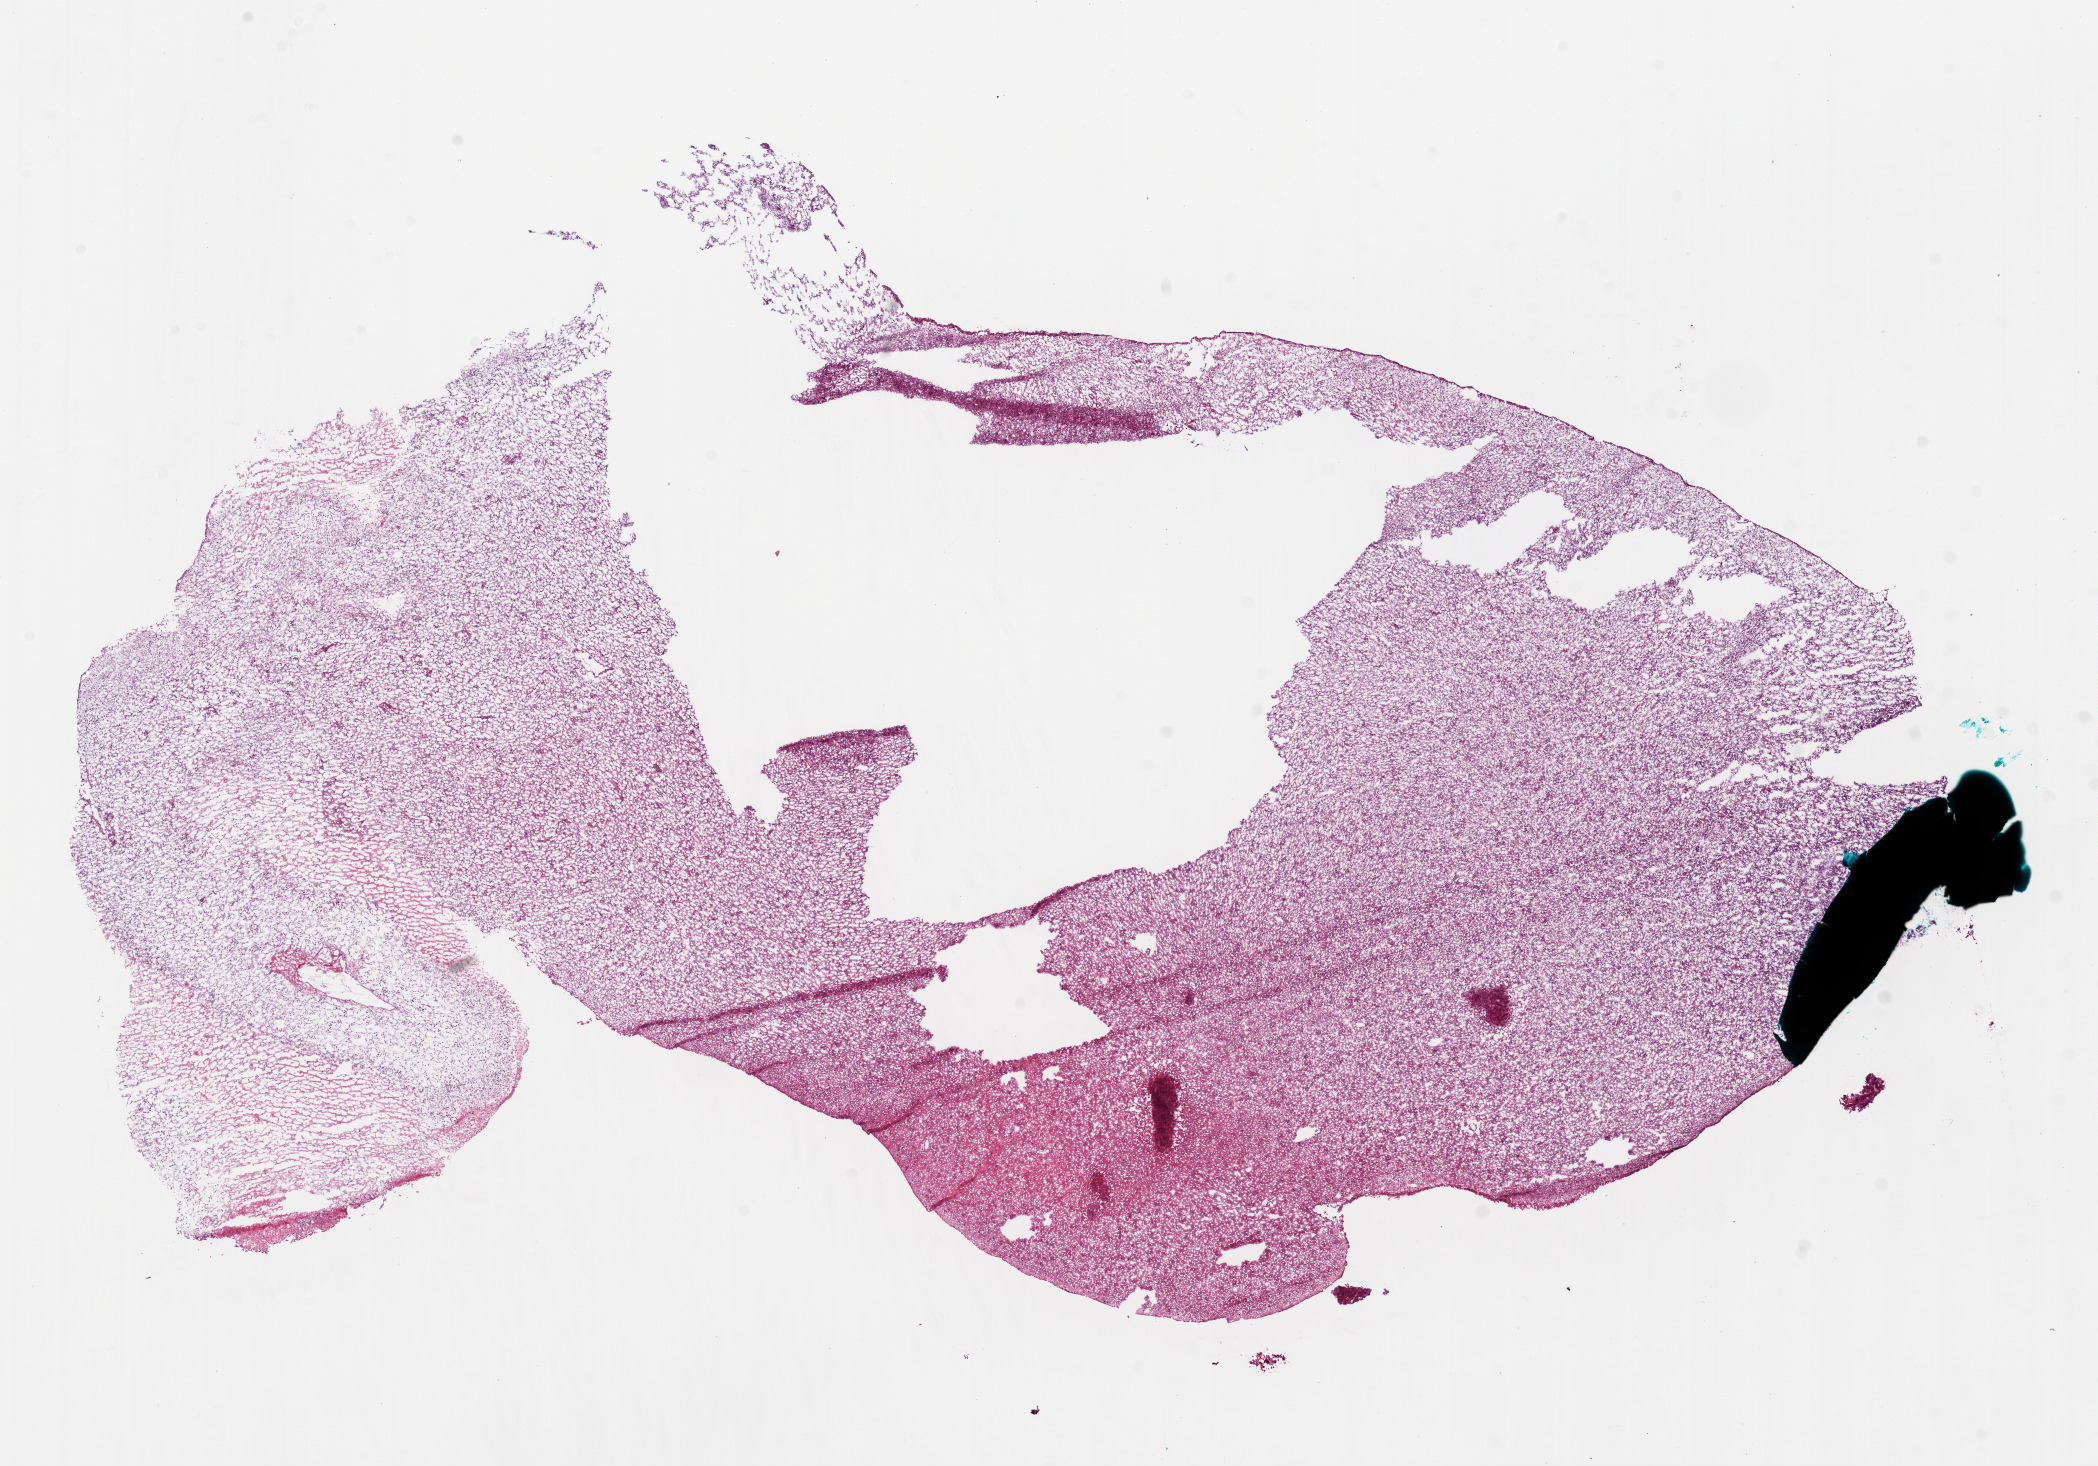
Digitized H&E tissue section (whole slide), a low-resolution overview of the entire scanned area, about 16.9 x 11.8 mm (acquisition: 20x scan), frozen section from the bottom of the tissue portion, brain, primary tumour sample. Female patient; age at initial diagnosis 51 years. Composition of this section per pathologist review: tumour cells 75%, tumour nuclei 100%, normal cells 0%, stromal cells 0%, necrosis 25%.
- diagnosis: Glioblastoma